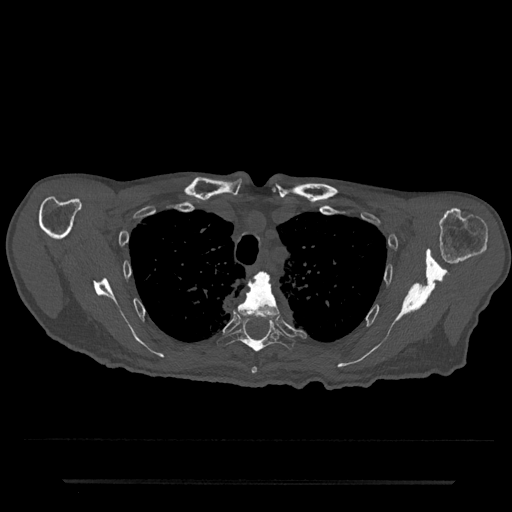
CT including the spine, one axial slice. Position 597 of 797 along the scan axis. Reconstruction kernel Br40s/3. 120 kVp. Bone window (W 1800 / L 400 HU). 0.5 mm slice thickness. 512 × 512 image matrix, field of view 427 × 427 mm. Male patient, age 74 years. Case-level facts recorded for this patient, not image findings: primary cancer: prostate.
Annotated regions visible in this slice (semi-automatically segmented with operator editing):
- T4 vertebra: bounding box [x1, y1, x2, y2] px = [237, 273, 280, 374]
- T5 vertebra: [217, 316, 295, 353]